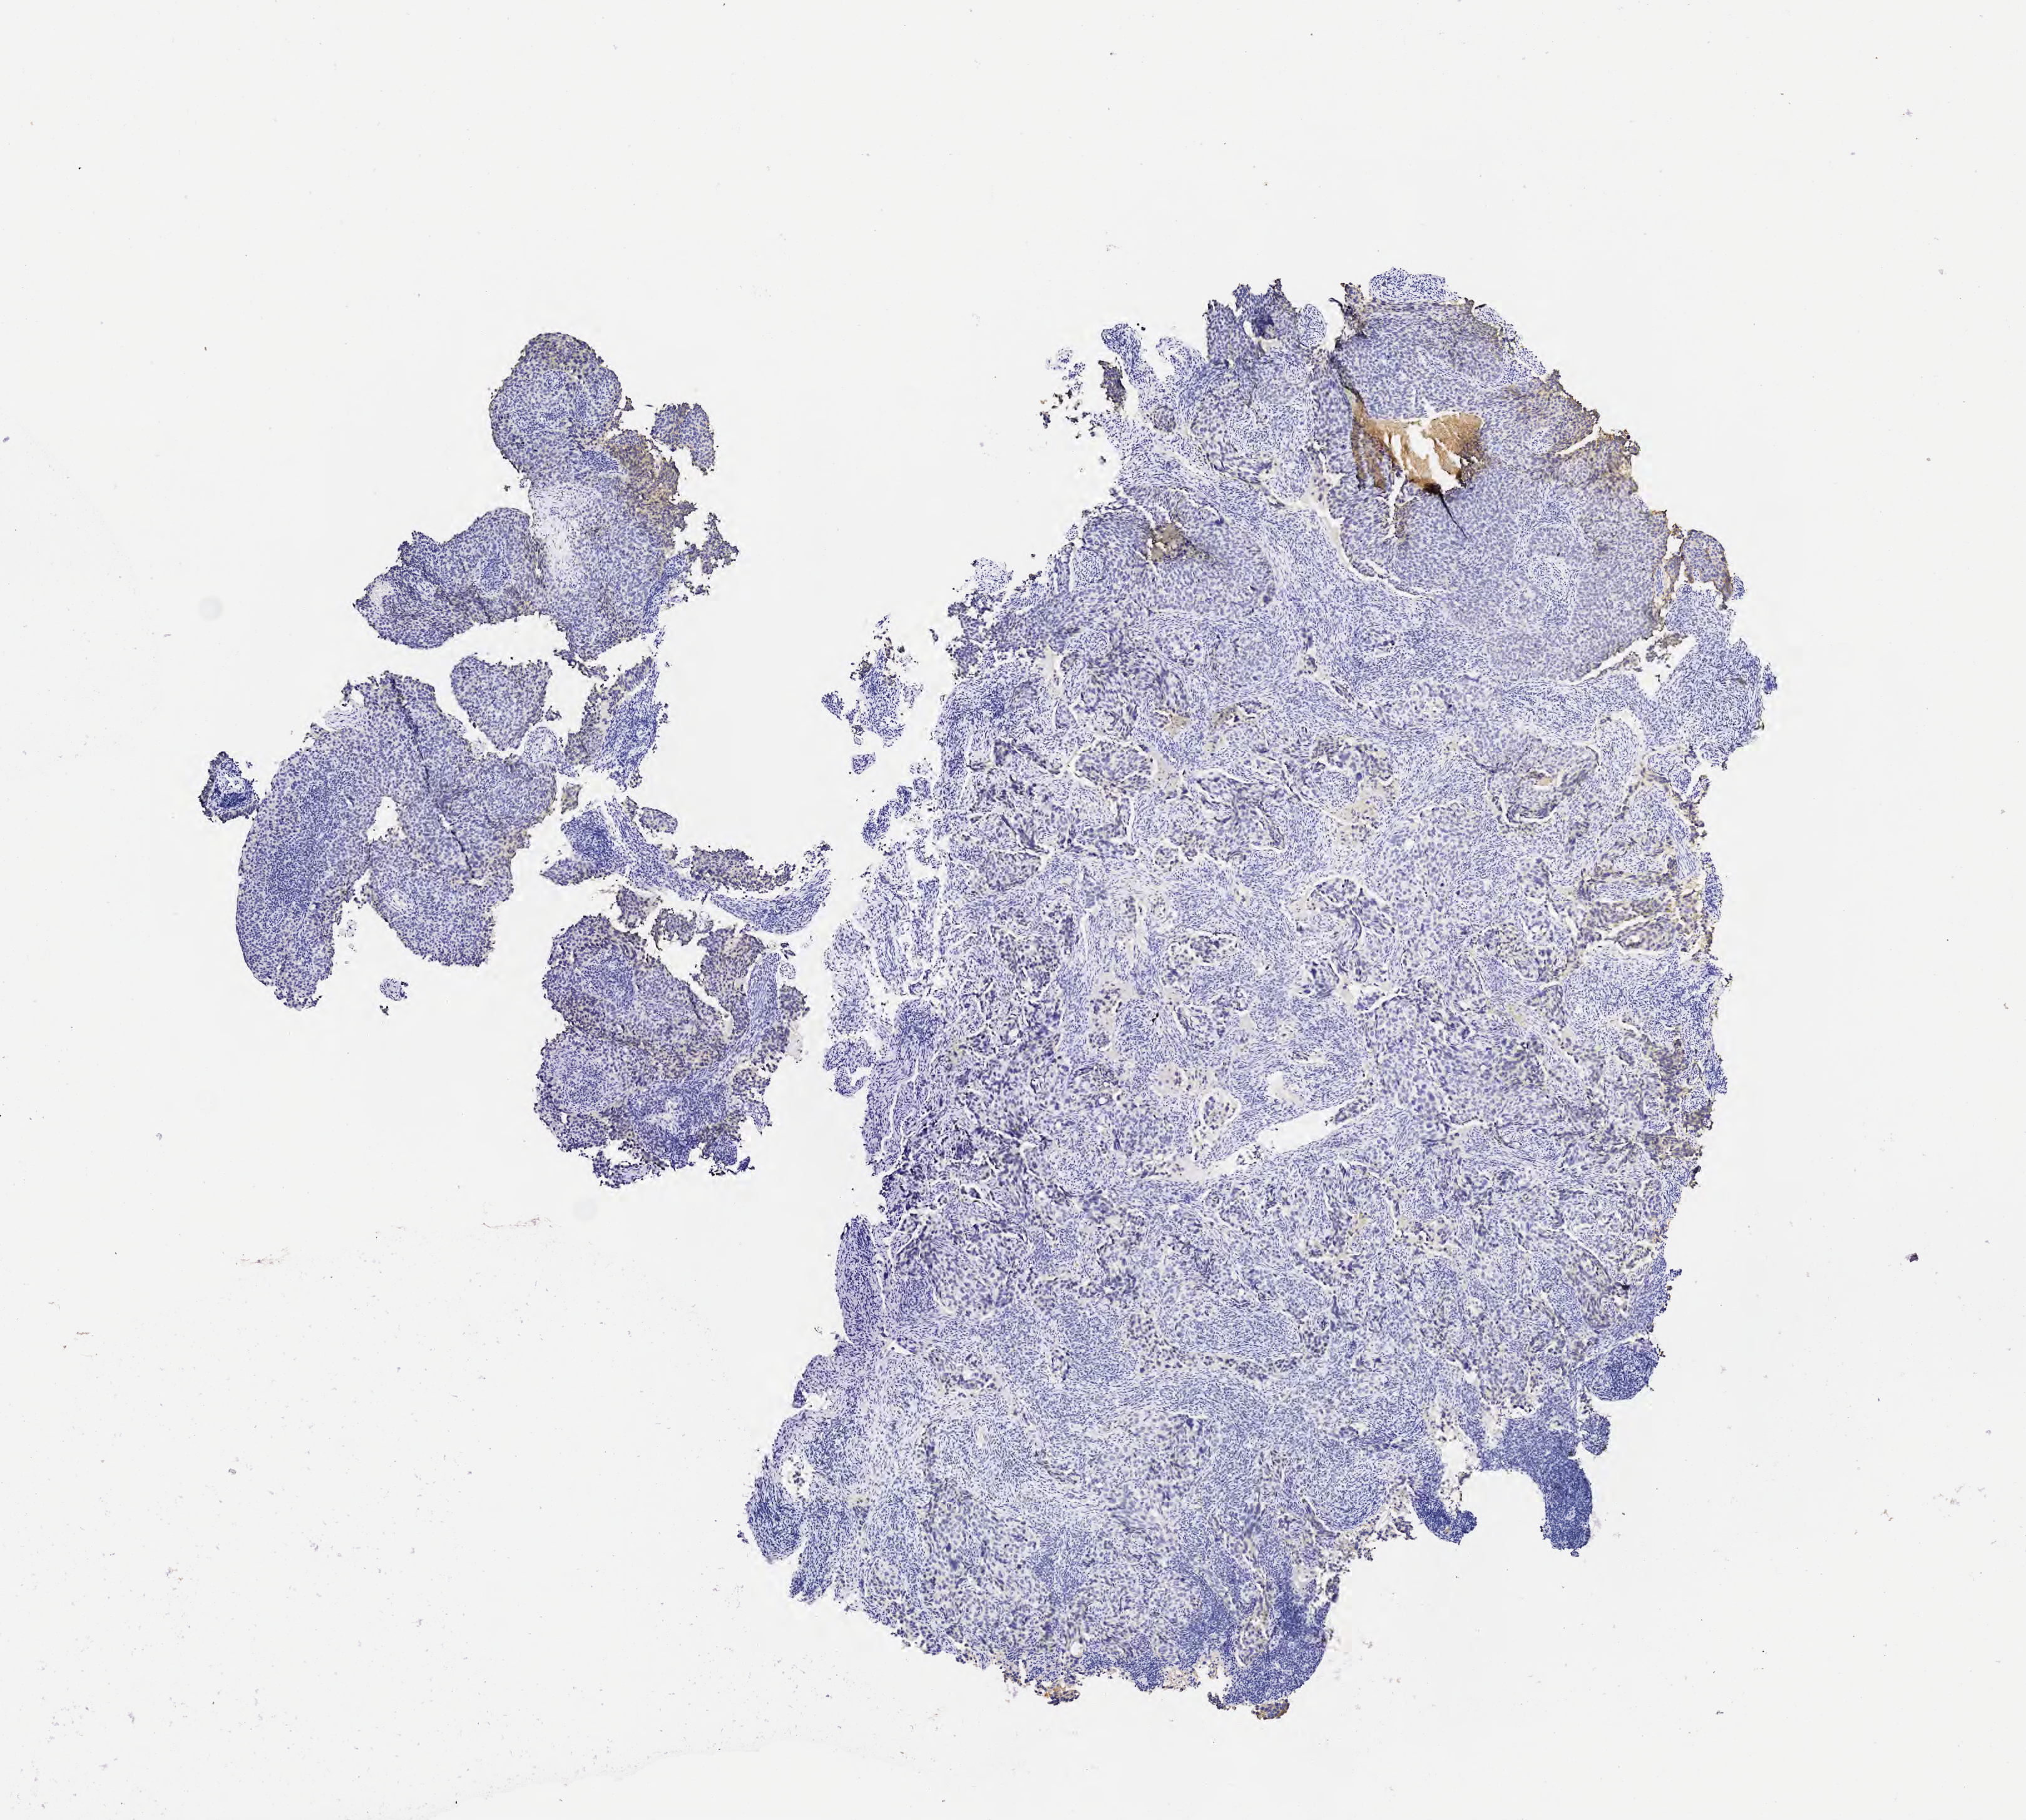
Immunohistochemistry (IHC) whole-slide image stained for MOC-31 (anti-EpCAM), low-resolution overview of the scanned area, about 6.5 x 5.9 mm. Tumor tissue. Anatomic site: cervix. Patient female; aged 47.
Histologic diagnosis: Squamous cell carcinoma, large cell, nonkeratinizing, NOS.